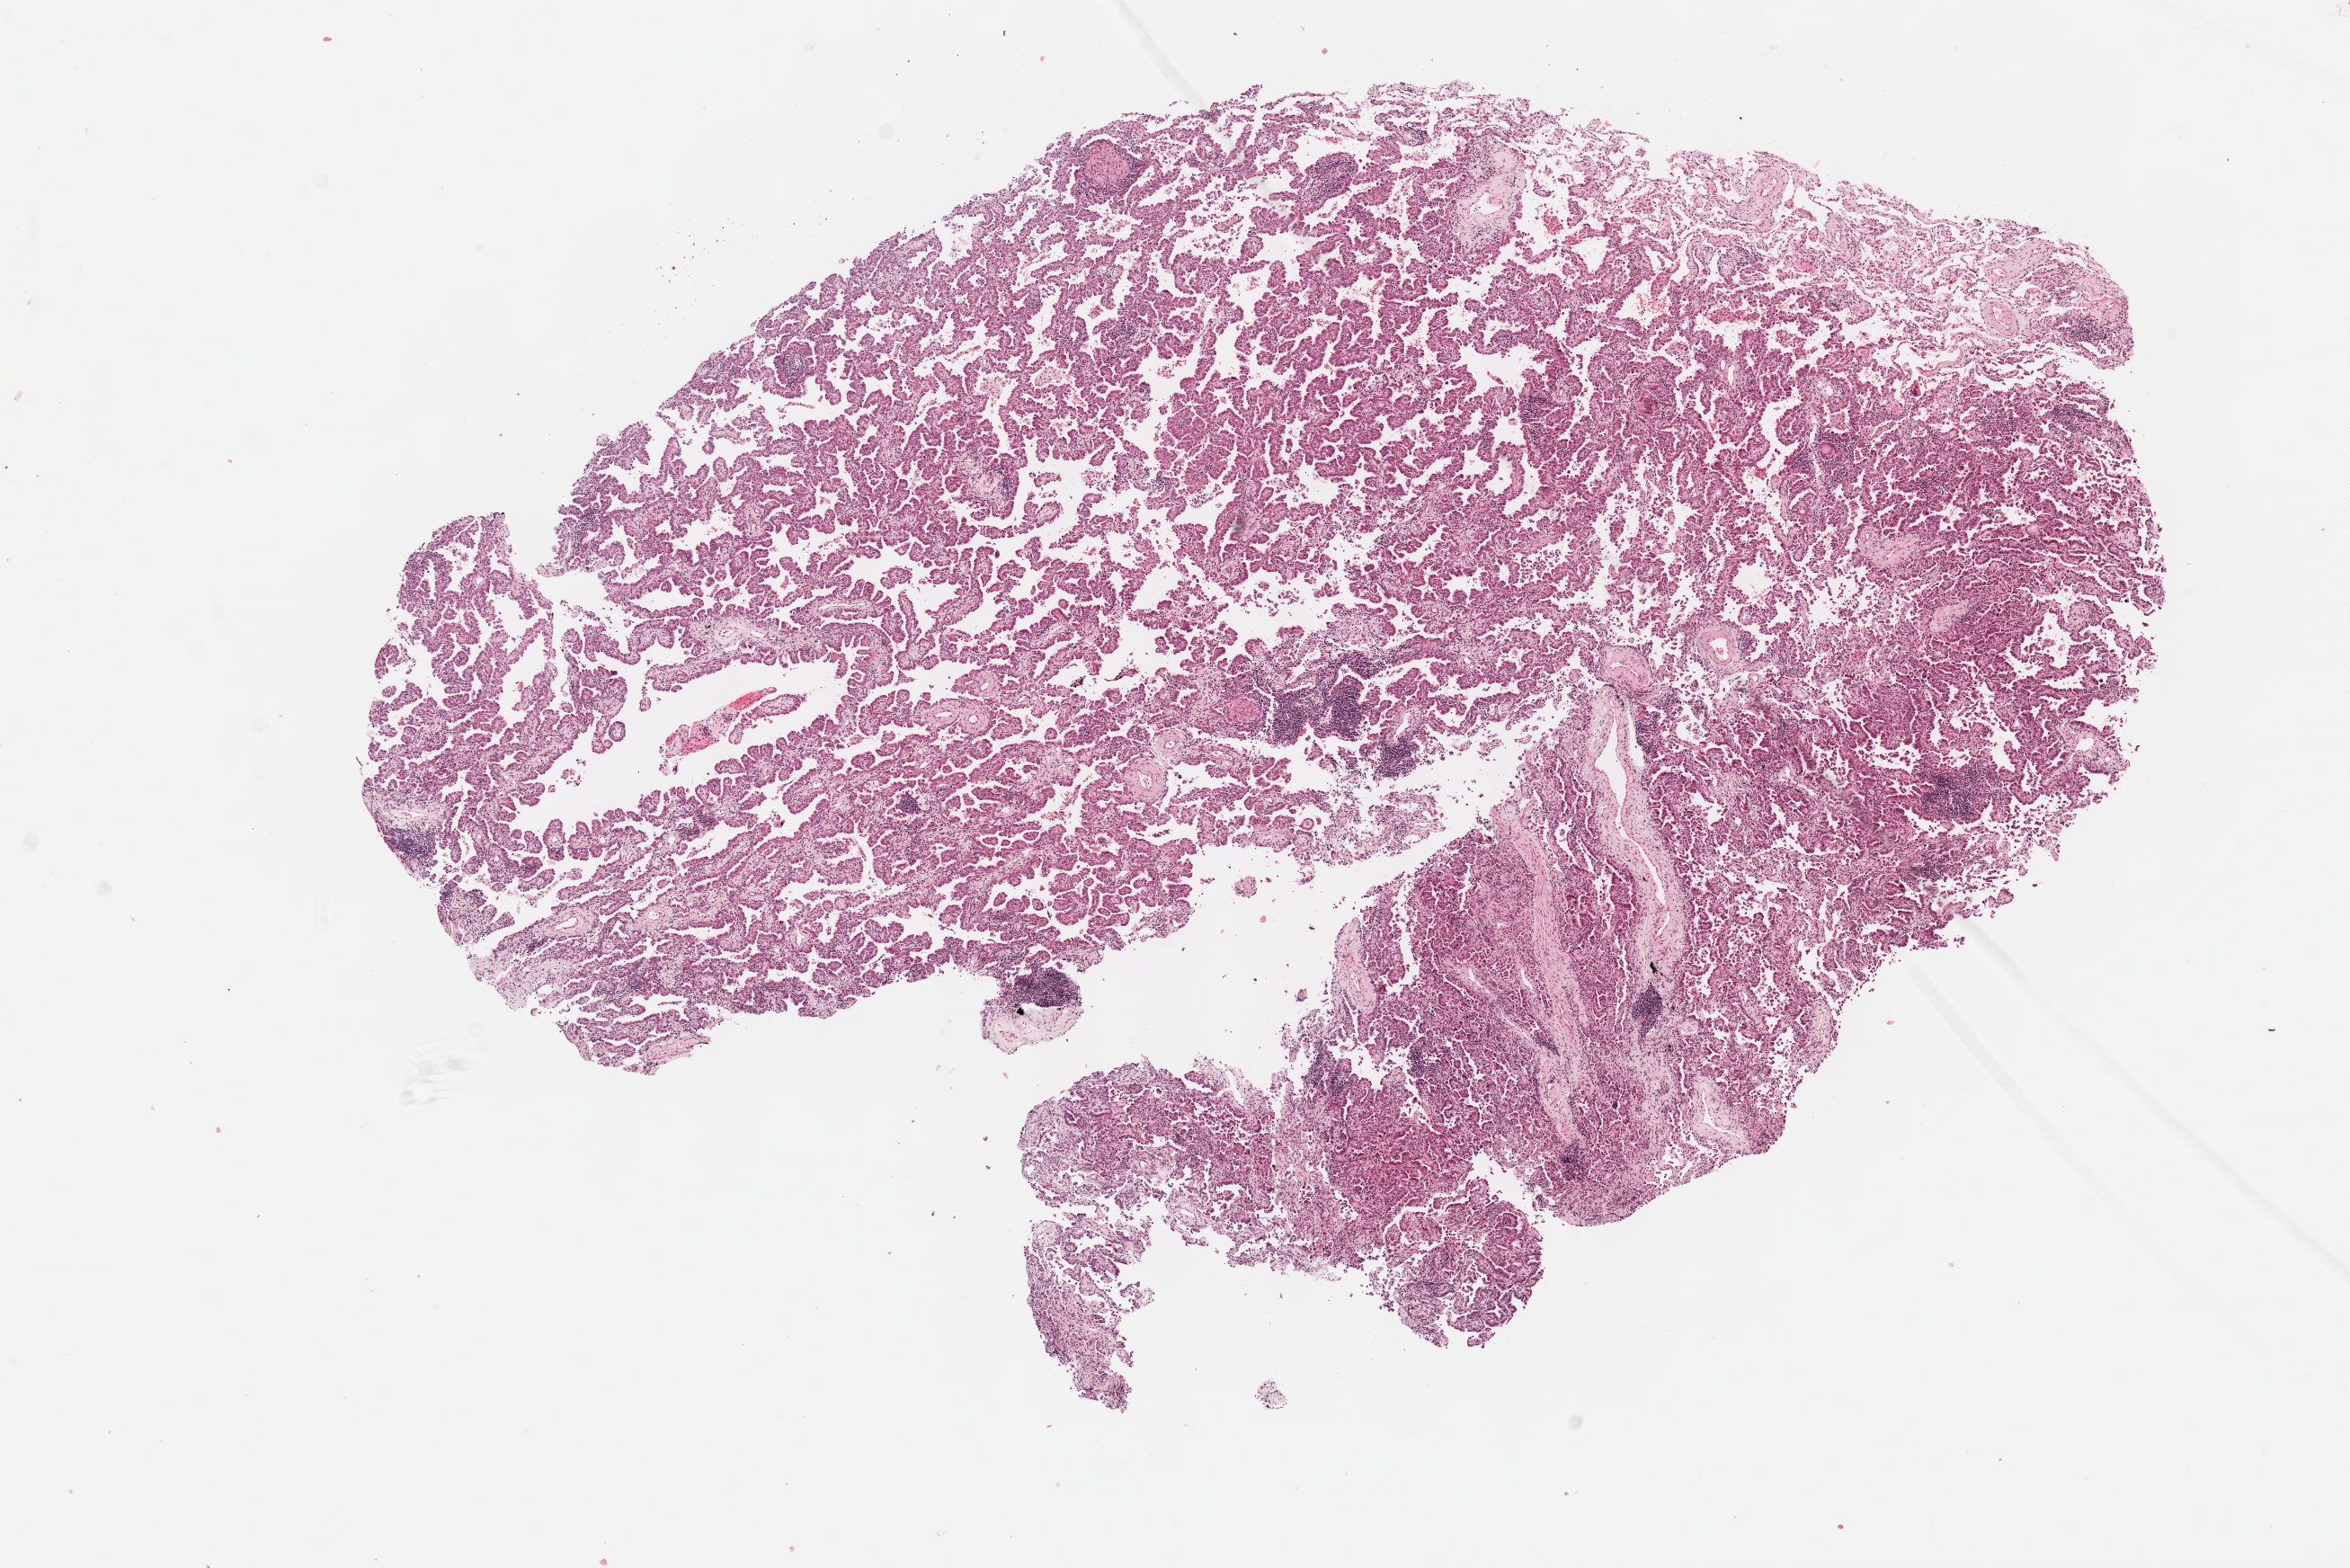
Whole-slide histology image, H&E — whole scanned area (about 10.6 x 7.1 mm, acquisition: 40x scan) shown as a low-resolution overview; FFPE section; sample: primary tumour, lung. Female patient; age at initial diagnosis 73 years.
Pathologic diagnosis: Adenocarcinoma, NOS.